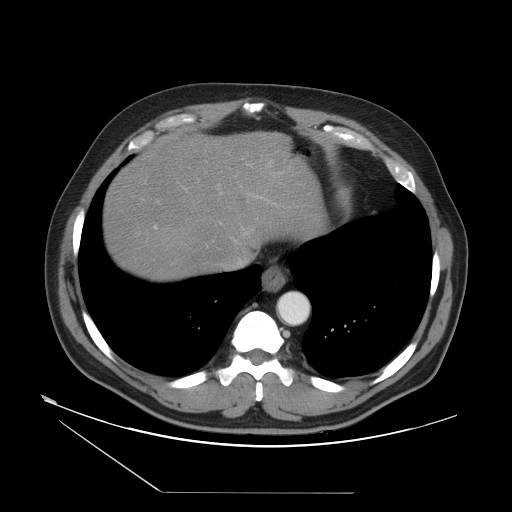
Contrast-enhanced abdominal CT, one axial slice; slice 45 of 55 in the series (ordered by position); reconstruction kernel STANDARD; intravenous contrast given; soft-tissue window (W 400 / L 40 HU); 512 × 512 image matrix, field of view 454 × 454 mm. Male patient, age 59 years. From the clinical record (not read from this slice): diagnosis: colorectal cancer liver metastases, imaged before liver resection; multiple liver metastases: yes; largest metastasis: 0.3 cm; chemotherapy before resection: yes.
Structures marked on this image (expert manual segmentation):
- hepatic veins: bounding box [x1, y1, x2, y2] px = [219, 187, 250, 262]
- liver: [107, 137, 318, 276]
- planned liver remnant (the part of the liver to remain after resection): [107, 165, 240, 276]
- portal vein (with intrahepatic branches): [142, 164, 277, 230]
- liver metastasis: [236, 195, 250, 210]